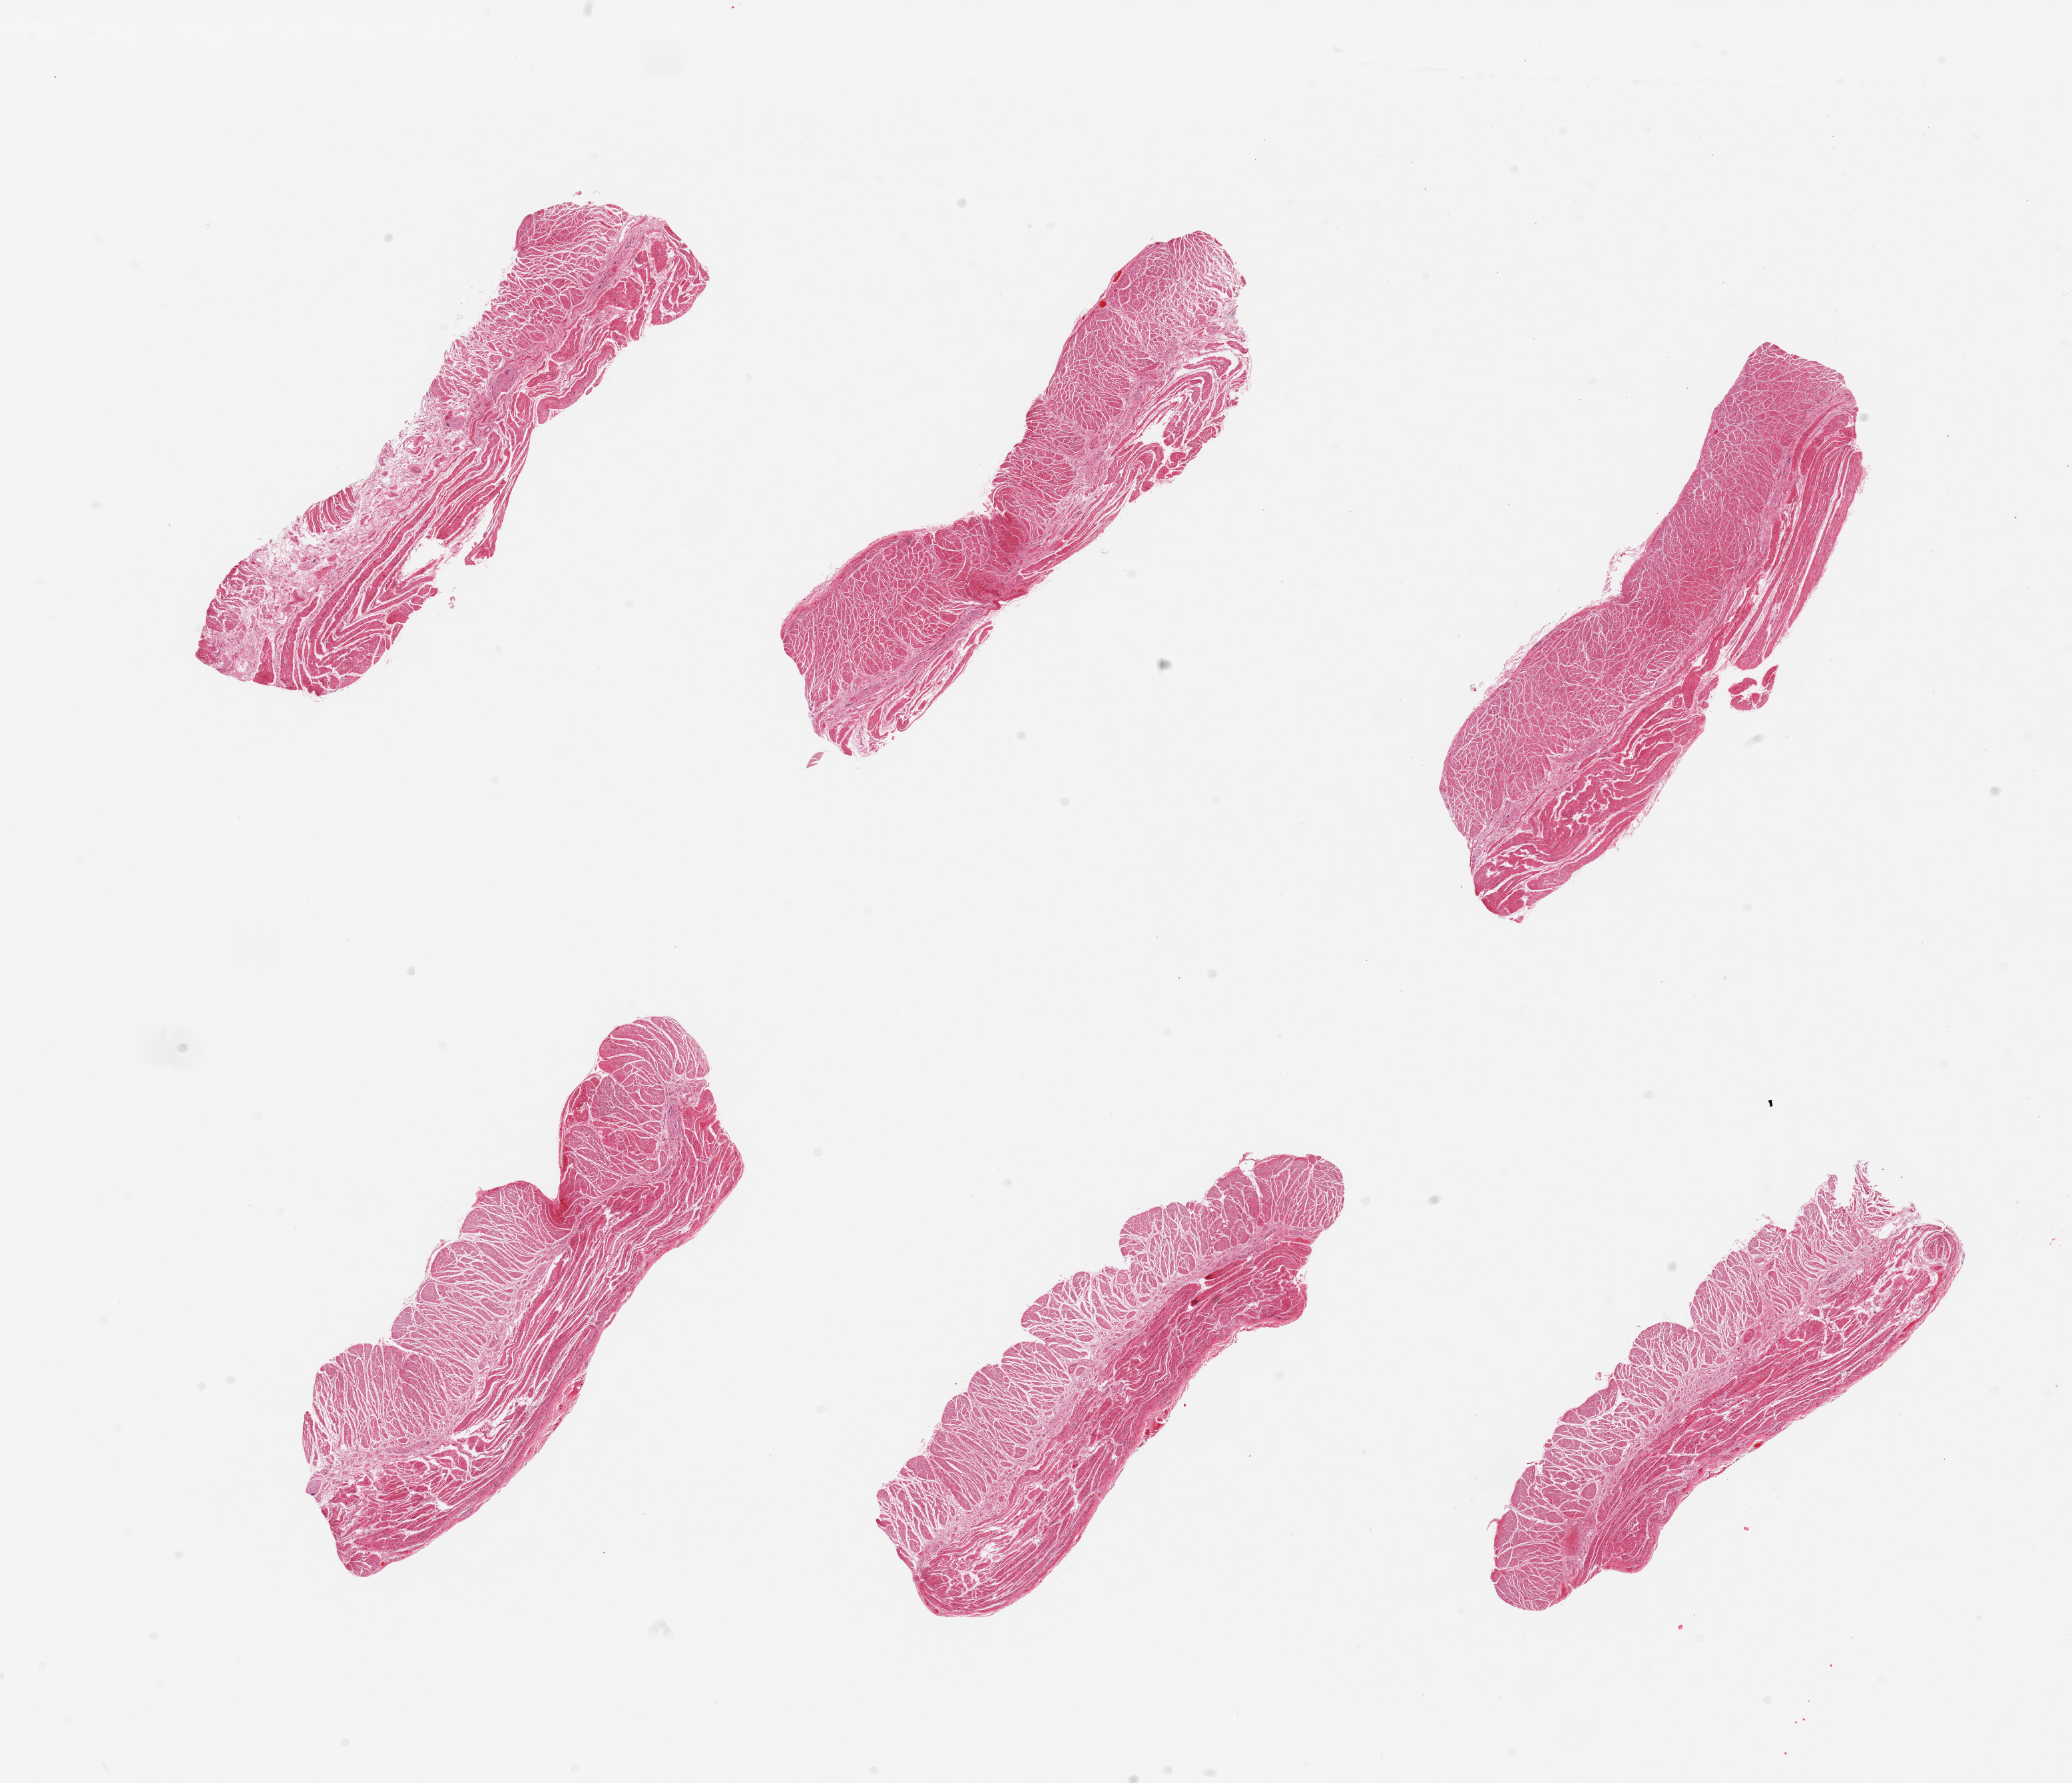
Digitized haematoxylin and eosin-stained section, brightfield, a low-resolution overview of the entire scanned area, about 24.6 x 21.2 mm (acquisition: 20x scan), PAXgene-fixed paraffin-embedded (PFPE) section, section of esophageal muscle (target tissue), tissue donor sample. Donor: male.
Pathologist's review note for this sample: 6 pieces; well trimmed.